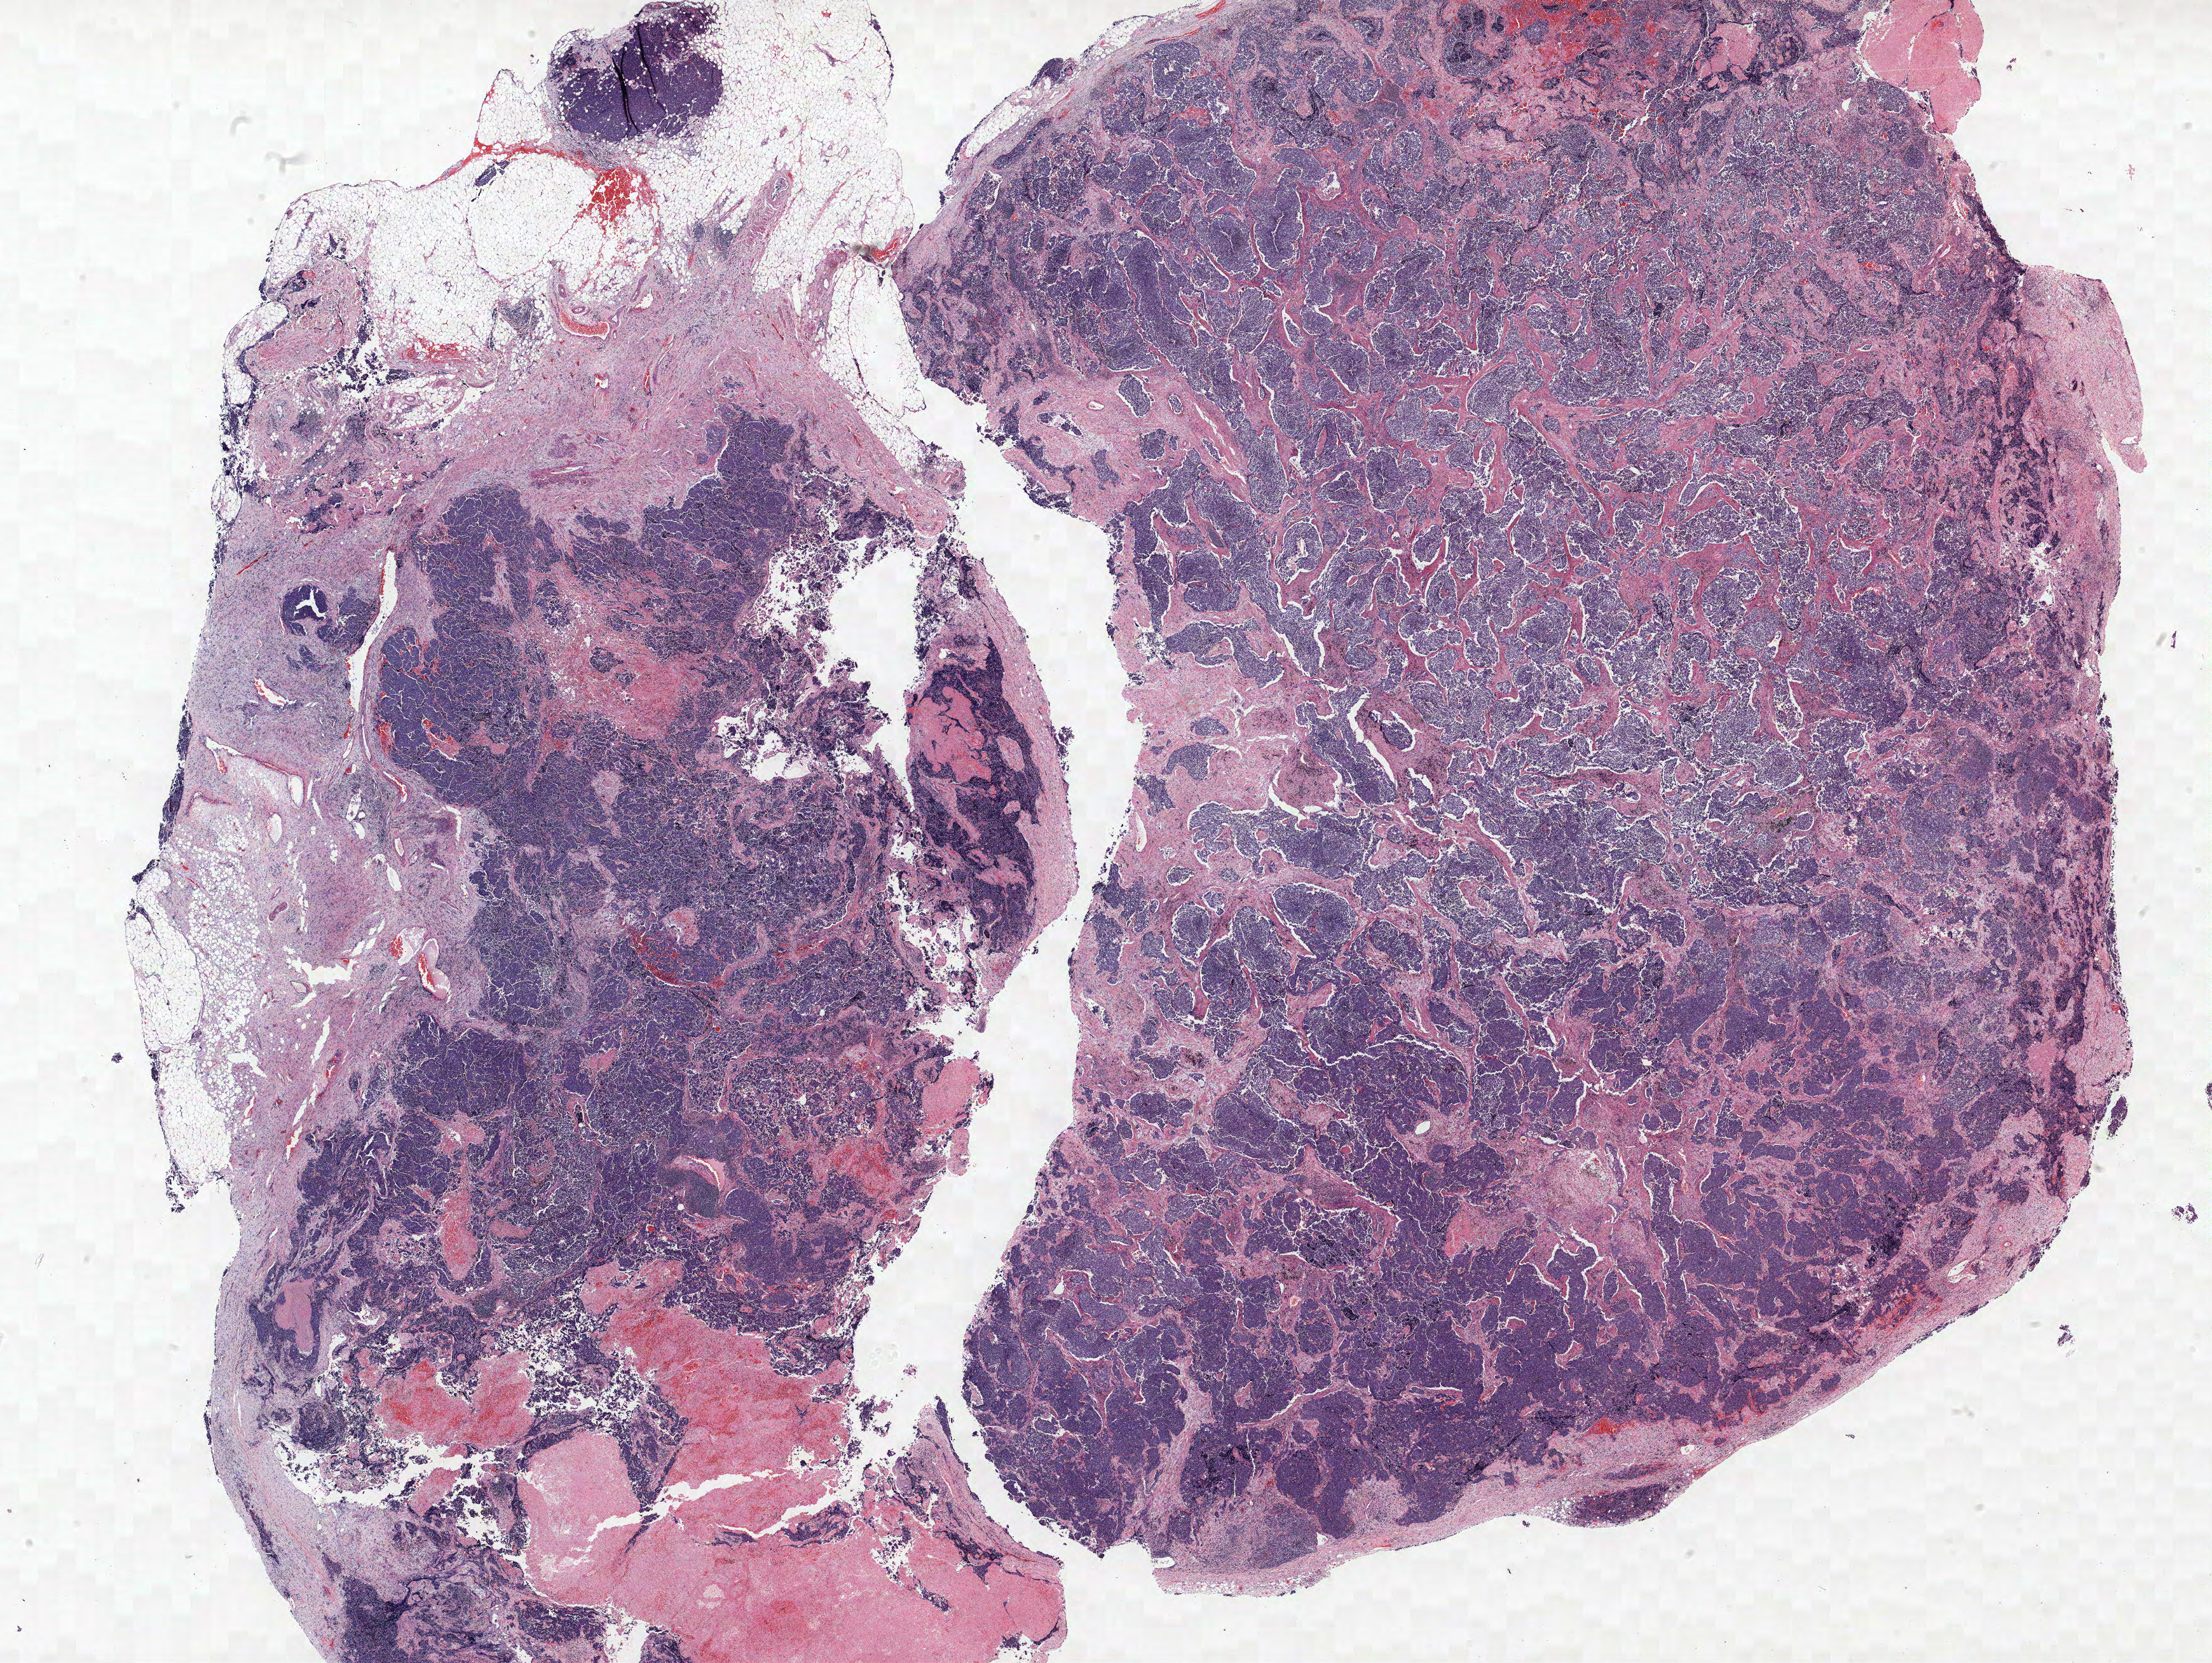
Whole-slide histology image, Hematoxylin and eosin (H&E) stained — low-resolution overview of the scanned area, about 27.8 x 20.9 mm, formalin-fixed paraffin-embedded (FFPE) section, lung tissue. Male patient, aged 73 at enrolment. Grade: cannot be assessed (GX).
• primary tumour location (clinical record): left upper lobe
• stage (AJCC 6th edition): IIIB
• participant's lung-cancer diagnosis: Small cell carcinoma, NOS
• tumour size (pathology): 19 mm